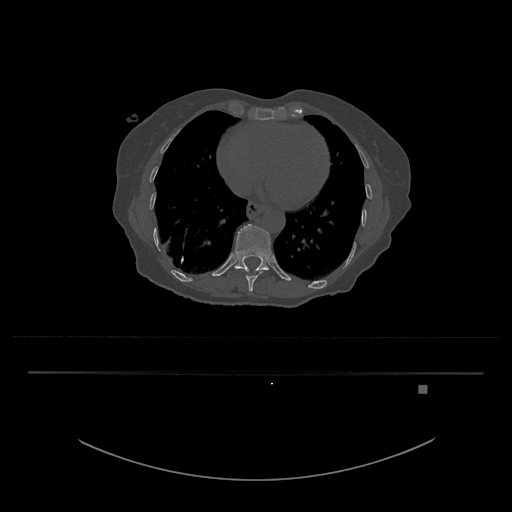
CT including the spine, one axial slice; position 686 of 797 along the scan axis; 120 kVp; bone window (W 1800 / L 400 HU); 0.5 mm slice thickness; 512 × 512 image matrix, field of view 500 × 500 mm. Female patient, age 57 years. From the clinical record (not read from this slice): primary cancer: cervical.
Outlined on this slice (semi-automatic segmentation, software-assisted and operator-edited):
- T10 vertebra: bounding box (x1, y1, x2, y2) in pixels: (241, 269, 263, 292)
- T11 vertebra: (228, 224, 271, 276)